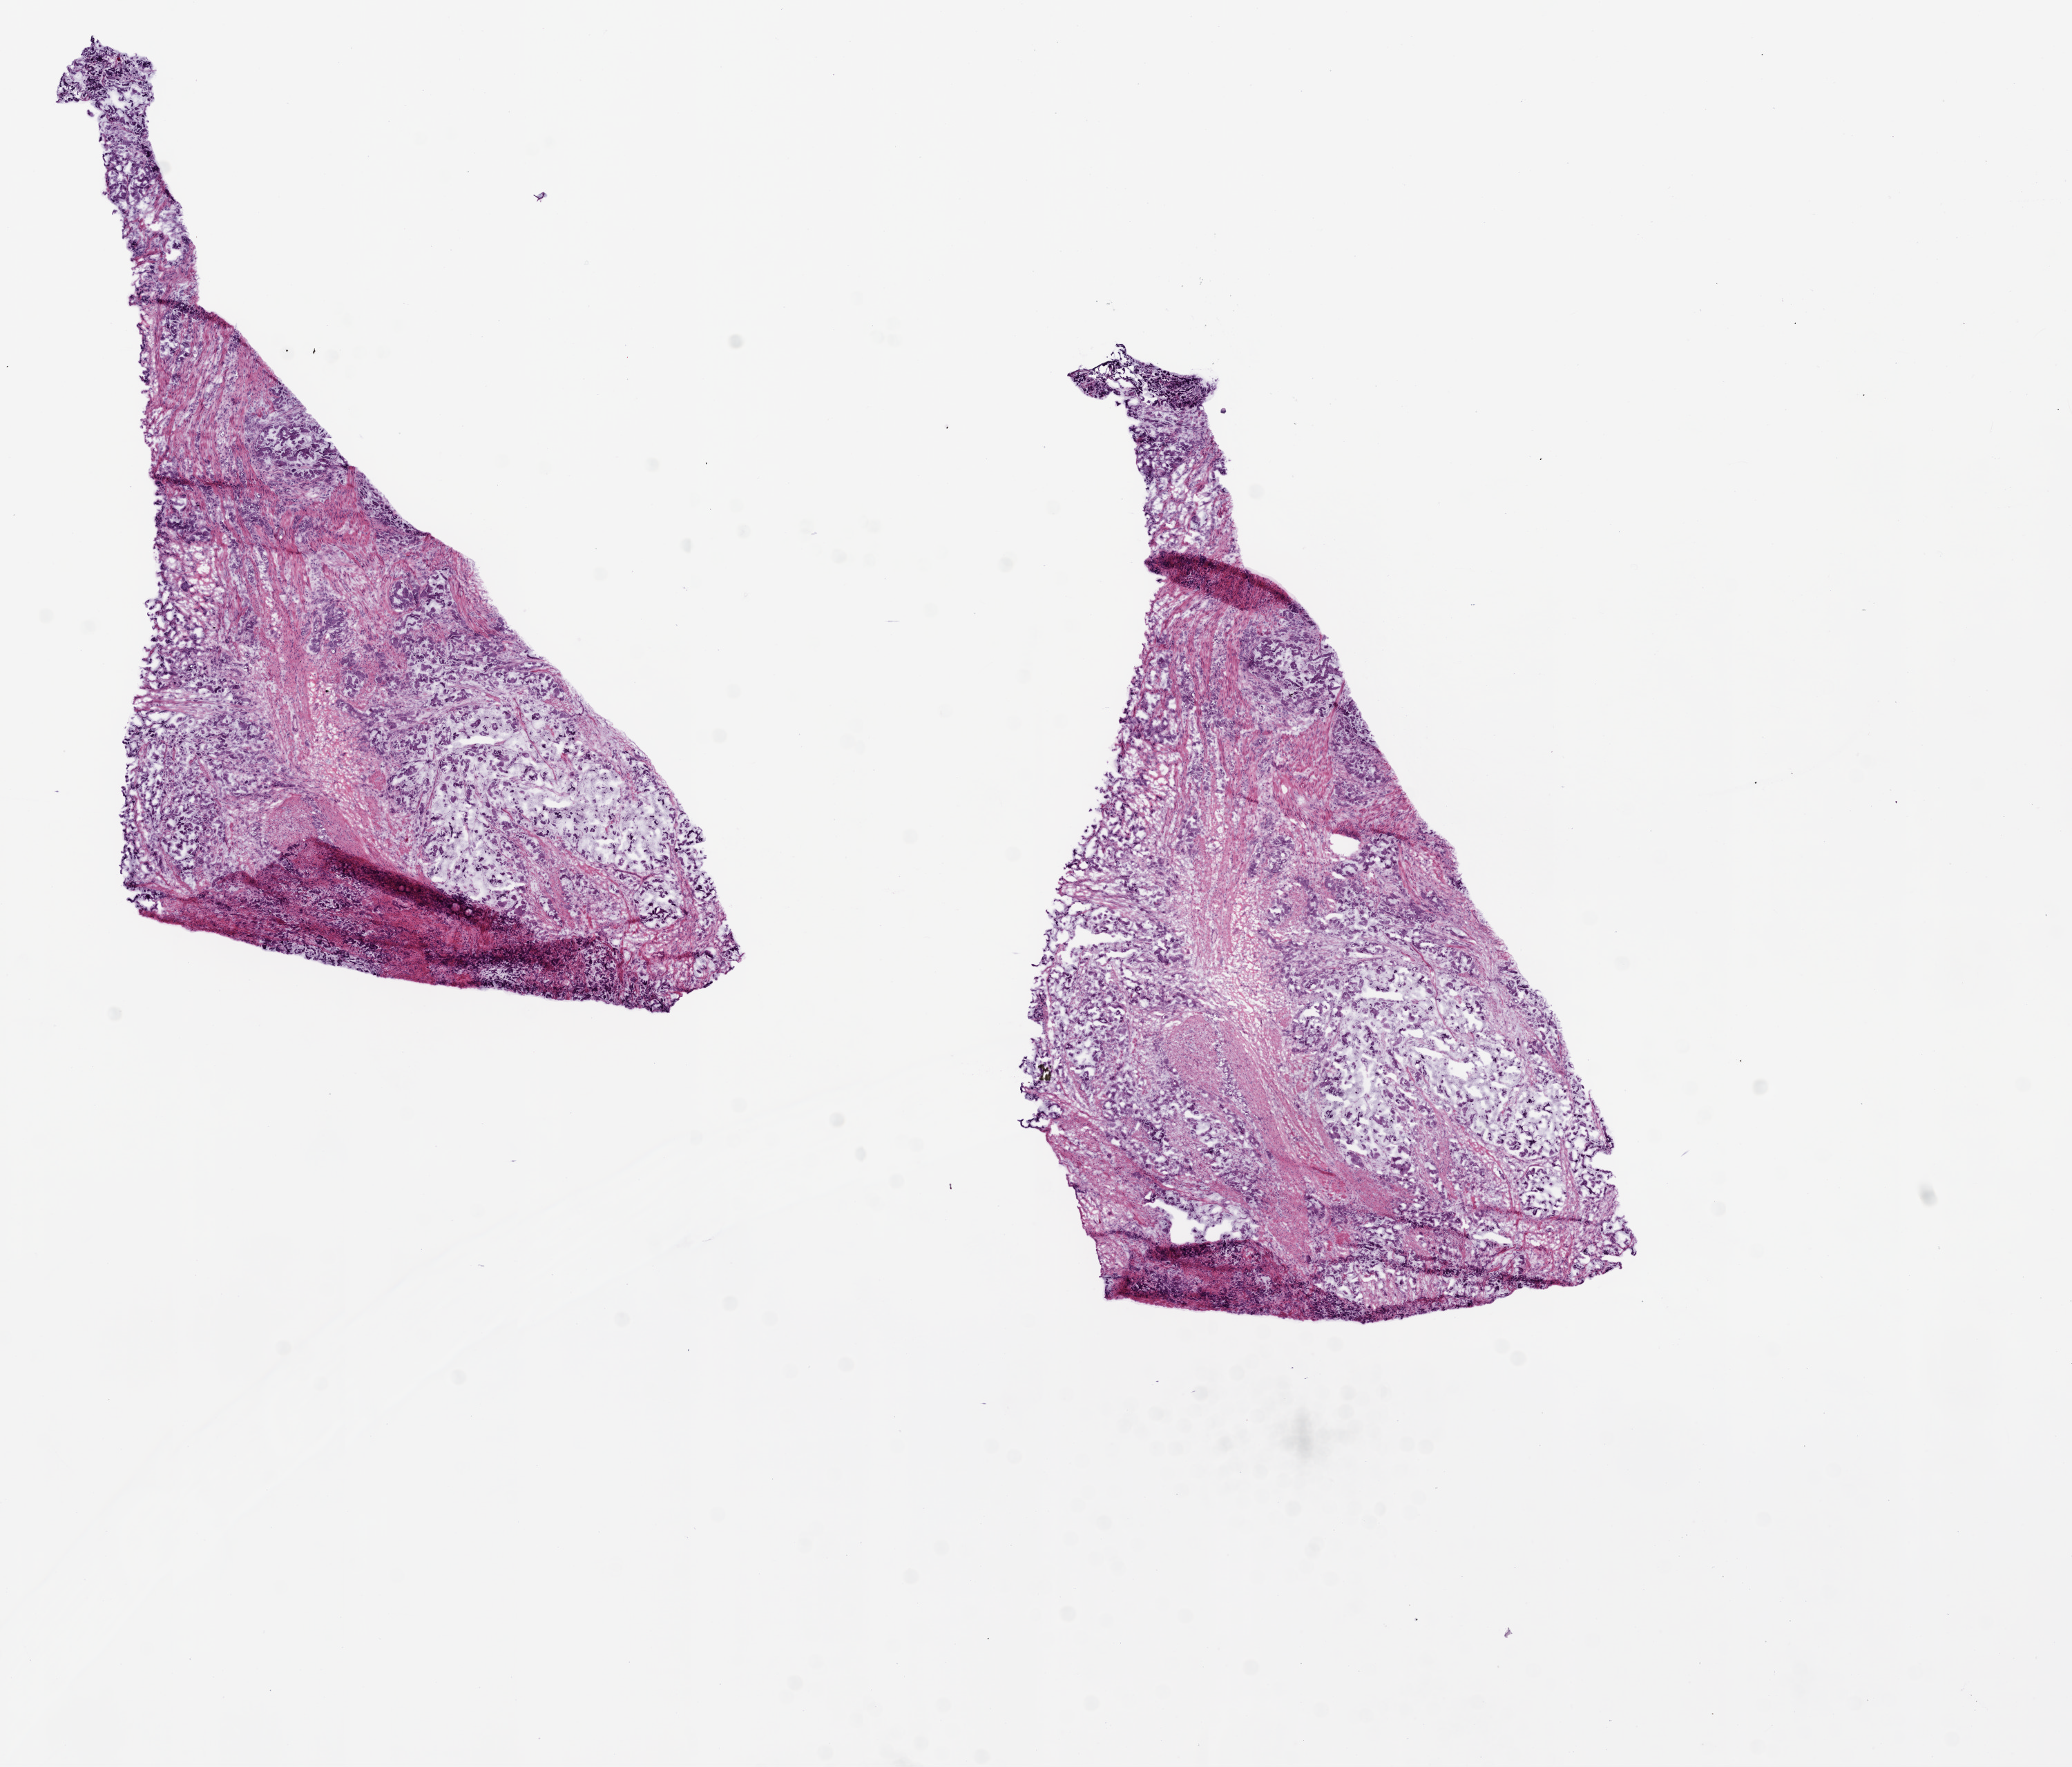
H&E whole-slide image, shown as a low-resolution overview of the whole scanned area (about 12.0 x 10.3 mm); frozen section from the bottom of the tissue portion; primary tumour sample from the stomach. Male, age 76 years at initial diagnosis. Histologic grade: G3 (poorly differentiated). Composition of this section per pathologist review: tumour cells 80%, tumour nuclei 70%, normal cells 0%, stromal cells 20%, necrosis 0%.
- pathologic diagnosis: Adenocarcinoma with mixed subtypes
- lymph nodes positive (case pathology): 2 of 20 examined
- TNM: T3 N1 M0
- AJCC pathologic stage: IIB (7th edition)